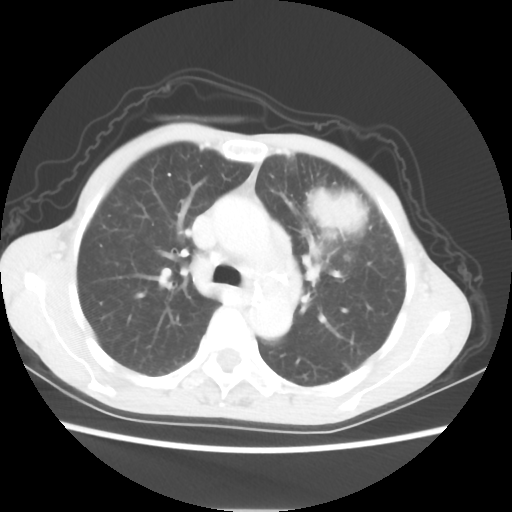
Chest CT, one axial slice. Position 40 of 56 along the scan axis. Reconstruction kernel STANDARD. 80 kVp. Lung window (W 1500 / L -600 HU). 5 mm slice thickness. 512 × 512 image matrix. Patient: female, 60 years. Case-level facts recorded for this patient, not image findings: clinical TNM (as recorded): T4 N1 M0.
Annotated regions visible in this slice (bounding box drawn by a radiologist):
- lung tumour (recorded histology: adenocarcinoma): bounding box [x1, y1, x2, y2] px = [306, 180, 364, 241]